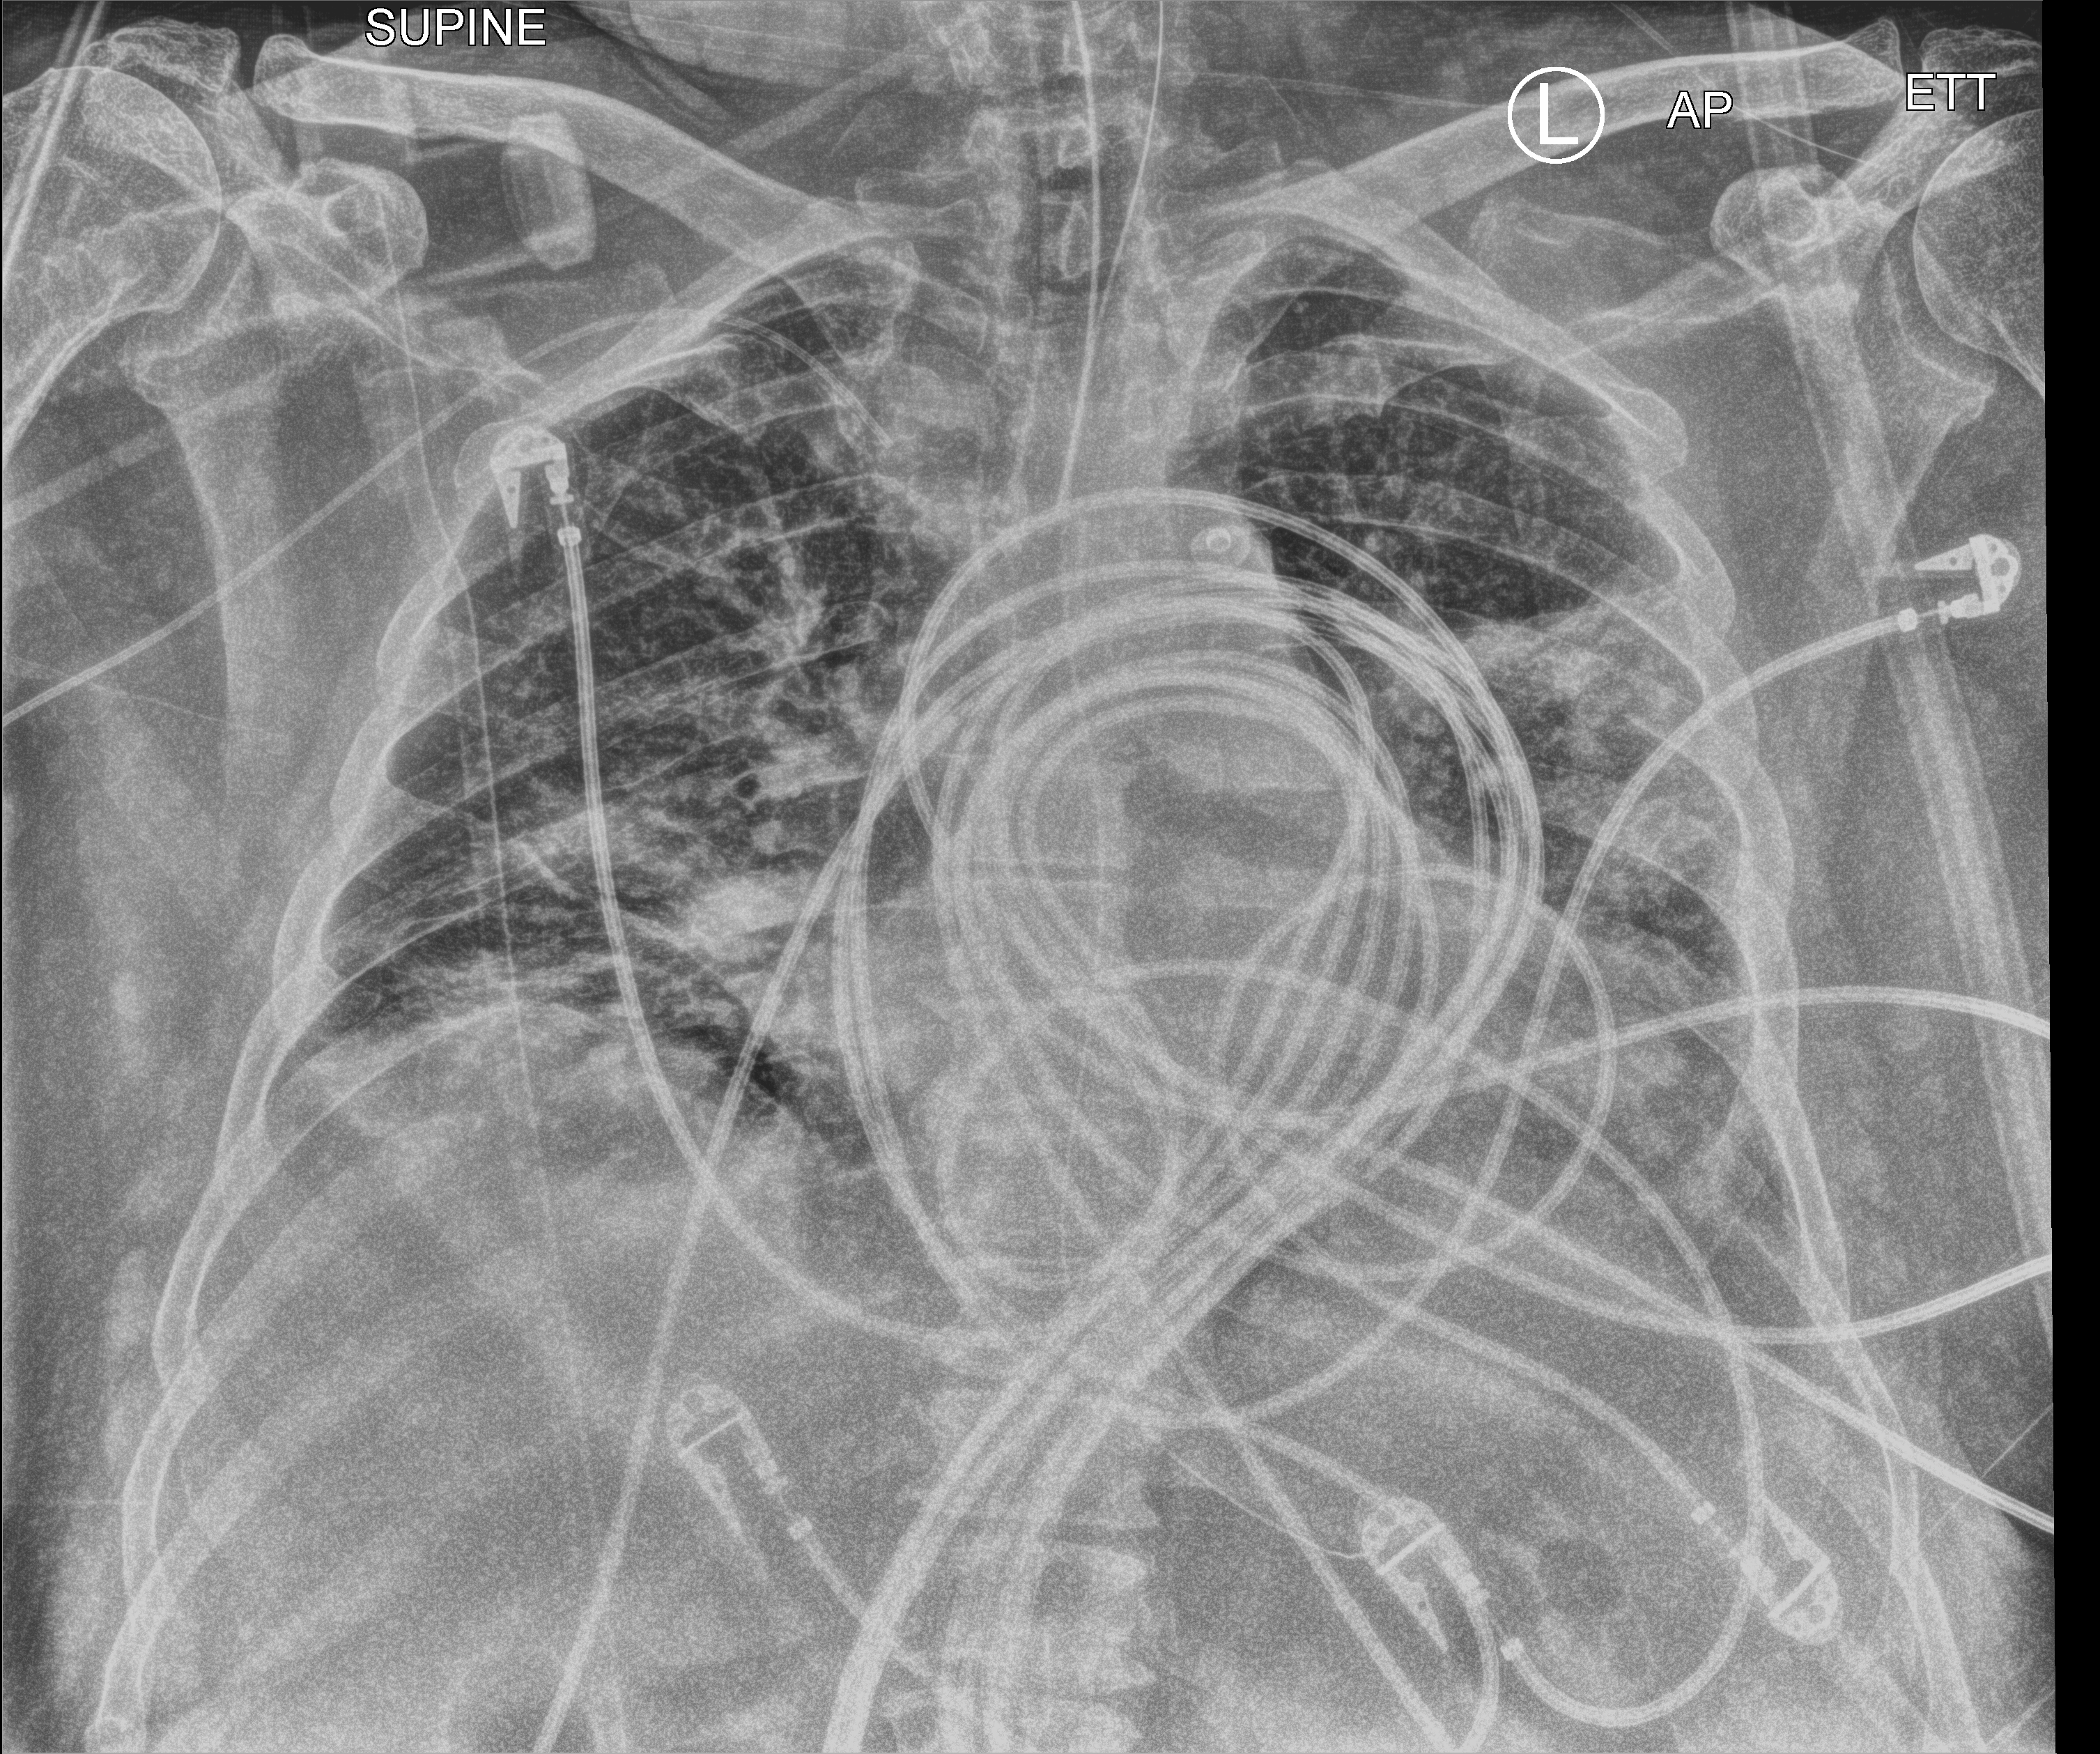
Chest X-ray (portable); anteroposterior (AP) projection. Male patient hospitalised with COVID-19, age 60–74 years.
Hospital-stay facts (about this admission, not read from this image; timing relative to this image not recorded):
- length of hospital stay: 26 days
- mechanically ventilated during this hospital stay: yes
- smoking status (admission record): never